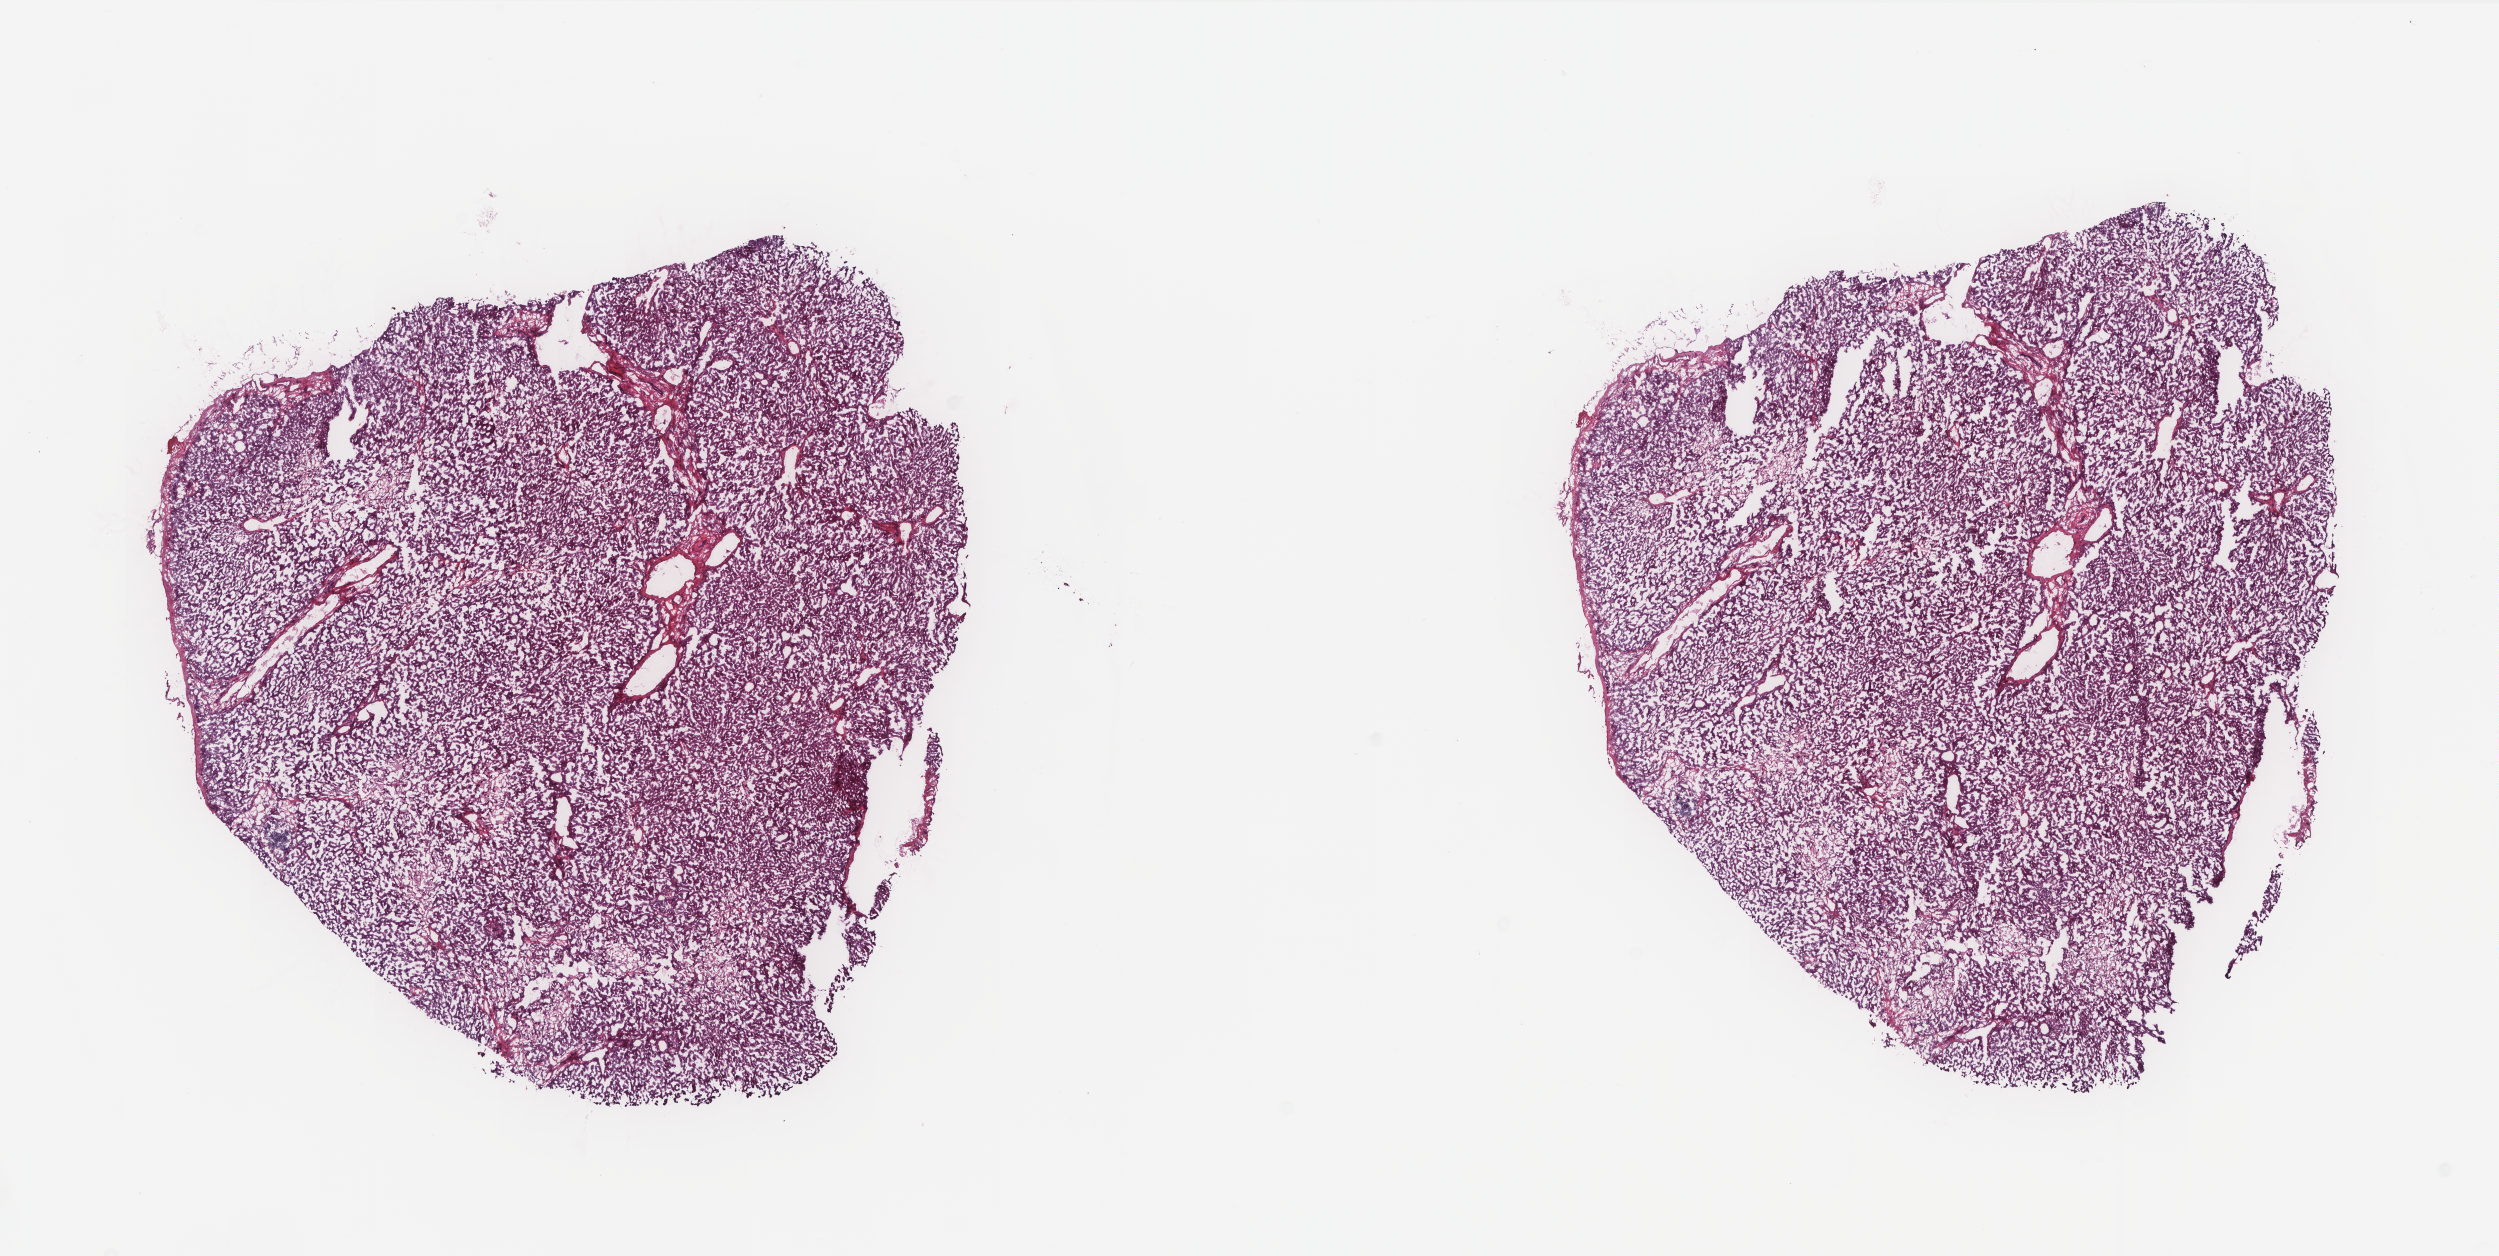
Digitized Hematoxylin and eosin (H&E) stained tissue section (whole slide) — whole scanned area (about 20.0 x 10.0 mm, slide scanned at 20x) shown as a low-resolution overview; frozen section from the top of the tissue portion; solid tissue normal (non-tumour tissue) sample from the liver. Male patient; age at initial diagnosis 45 years. Slide review estimates, as recorded: tumour cells 0%, tumour nuclei 0%, normal cells 100%, stromal cells 0%, necrosis 0%. Infiltration values recorded for this section: lymphocyte infiltration 0%, monocyte infiltration 0%, neutrophil infiltration 0%.
This section: solid tissue normal sample (biorepository sample class). Patient diagnosis: Hepatocellular carcinoma, NOS.